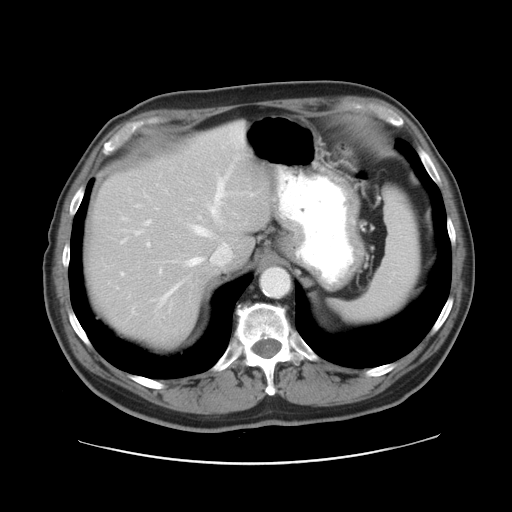
Contrast-enhanced abdominal CT, one axial slice. Slice 22 of 28 in the series (ordered by position). Reconstruction kernel STANDARD. 120 kVp. Intravenous contrast given. Soft-tissue window (W 400 / L 40 HU). 7.5 mm slice thickness. 512 × 512 image matrix, field of view 402 × 402 mm. Male patient, age 74 years. Case-level facts recorded for this patient, not image findings: diagnosis: colorectal cancer liver metastases, imaged before liver resection; multiple liver metastases: no; largest metastasis: 5 cm; chemotherapy before resection: yes.
Structures marked on this image (expert manual segmentation):
- hepatic veins: bounding box (x1, y1, x2, y2) in pixels: (121, 176, 227, 300)
- liver: (89, 127, 271, 342)
- planned liver remnant (the part of the liver to remain after resection): (89, 179, 215, 341)
- portal vein (with intrahepatic branches): (146, 221, 151, 224)